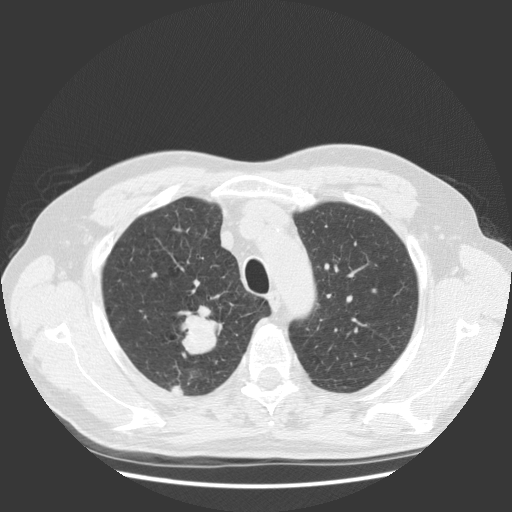
Low-dose screening chest CT, axial slice. Baseline screening round. Lung window (W 1500 / L -600 HU). Standard (soft-tissue) reconstruction kernel (STANDARD). Male participant, aged 63 years at enrolment. Current smoker at enrolment.
Expert-annotated lung lesion, box from (x=159, y=306) to (x=231, y=378) px. The screening reader recorded 2 non-calcified nodules or masses ≥4 mm on this exam (right upper lobe, right upper lobe); which of them this box marks is not recorded. Official screen result: positive, change unspecified: nodule(s) >= 4 mm or enlarging nodule(s), mass(es), or other non-specific abnormalities suspicious for lung cancer. Later outcome: lung cancer diagnosed 30 days after this screen — squamous cell carcinoma, NOS, right upper lobe, stage IIIB (AJCC 6th edition), 35 mm at pathology.